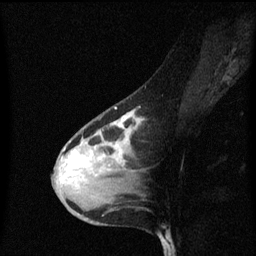
Breast MRI (dynamic contrast-enhanced), one sagittal slice. Position 39 of 60 along the scan axis. Dynamic contrast-enhanced series, image 2 of 3 at this slice position (ordered by acquisition). 1.5 T. TE 4.2 ms, TR 8.4 ms. 256 × 256 image matrix, field of view 200 × 200 mm. Female patient, age 38 years. From the clinical record (not read from this slice): setting: breast cancer imaged before/during neoadjuvant chemotherapy; receptor status: HR-positive, HER2-negative.
Structures marked on this image (semi-automatic segmentation, software-assisted and operator-edited):
- analysis volume of interest (the breast-tissue region the enhancement analysis was run in; not a lesion): bounding box (x1, y1, x2, y2) in pixels: (52, 102, 143, 205)
- tumour enhancement mask (voxels above the 70 % enhancement threshold inside the analysis volume of interest): (64, 112, 141, 177)